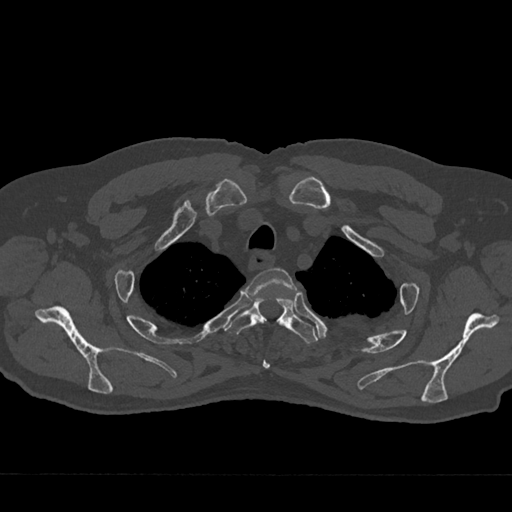
CT including the spine, one axial slice; slice 584 of 797 in the series (ordered by position); reconstruction kernel Br40s/3; bone window (W 1800 / L 400 HU); 512 × 512 image matrix, field of view 377 × 377 mm. Patient: male, 75 years. From the clinical record (not read from this slice): primary cancer: renal; vertebrae with lytic lesions (as recorded): T4.
Outlined on this slice (semi-automatically segmented with operator editing):
- T2 vertebra: box from (x=248, y=268) to (x=296, y=369) px
- T3 vertebra: (x=226, y=297)–(x=318, y=344)